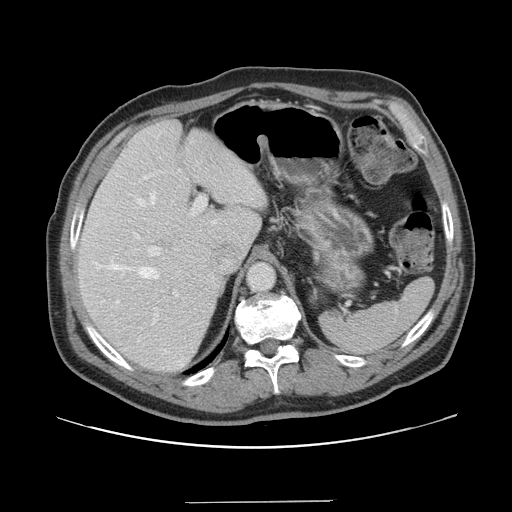
Contrast-enhanced abdominal CT, one axial slice. Slice 106 of 151 in the series (ordered by position). Intravenous contrast given. Soft-tissue window (W 400 / L 40 HU). 2.5 mm slice thickness. 512 × 512 image matrix. Male patient, age 63 years. Case-level facts recorded for this patient, not image findings: diagnosis: colorectal cancer liver metastases, imaged before liver resection; multiple liver metastases: no; largest metastasis: 2.1 cm; disease in both lobes: no.
Annotated regions visible in this slice (expert manual segmentation):
- hepatic veins: bounding box [x1, y1, x2, y2] px = [107, 191, 215, 279]
- liver: [78, 120, 267, 373]
- planned liver remnant (the part of the liver to remain after resection): [78, 120, 262, 373]
- portal vein (with intrahepatic branches): [148, 170, 206, 316]